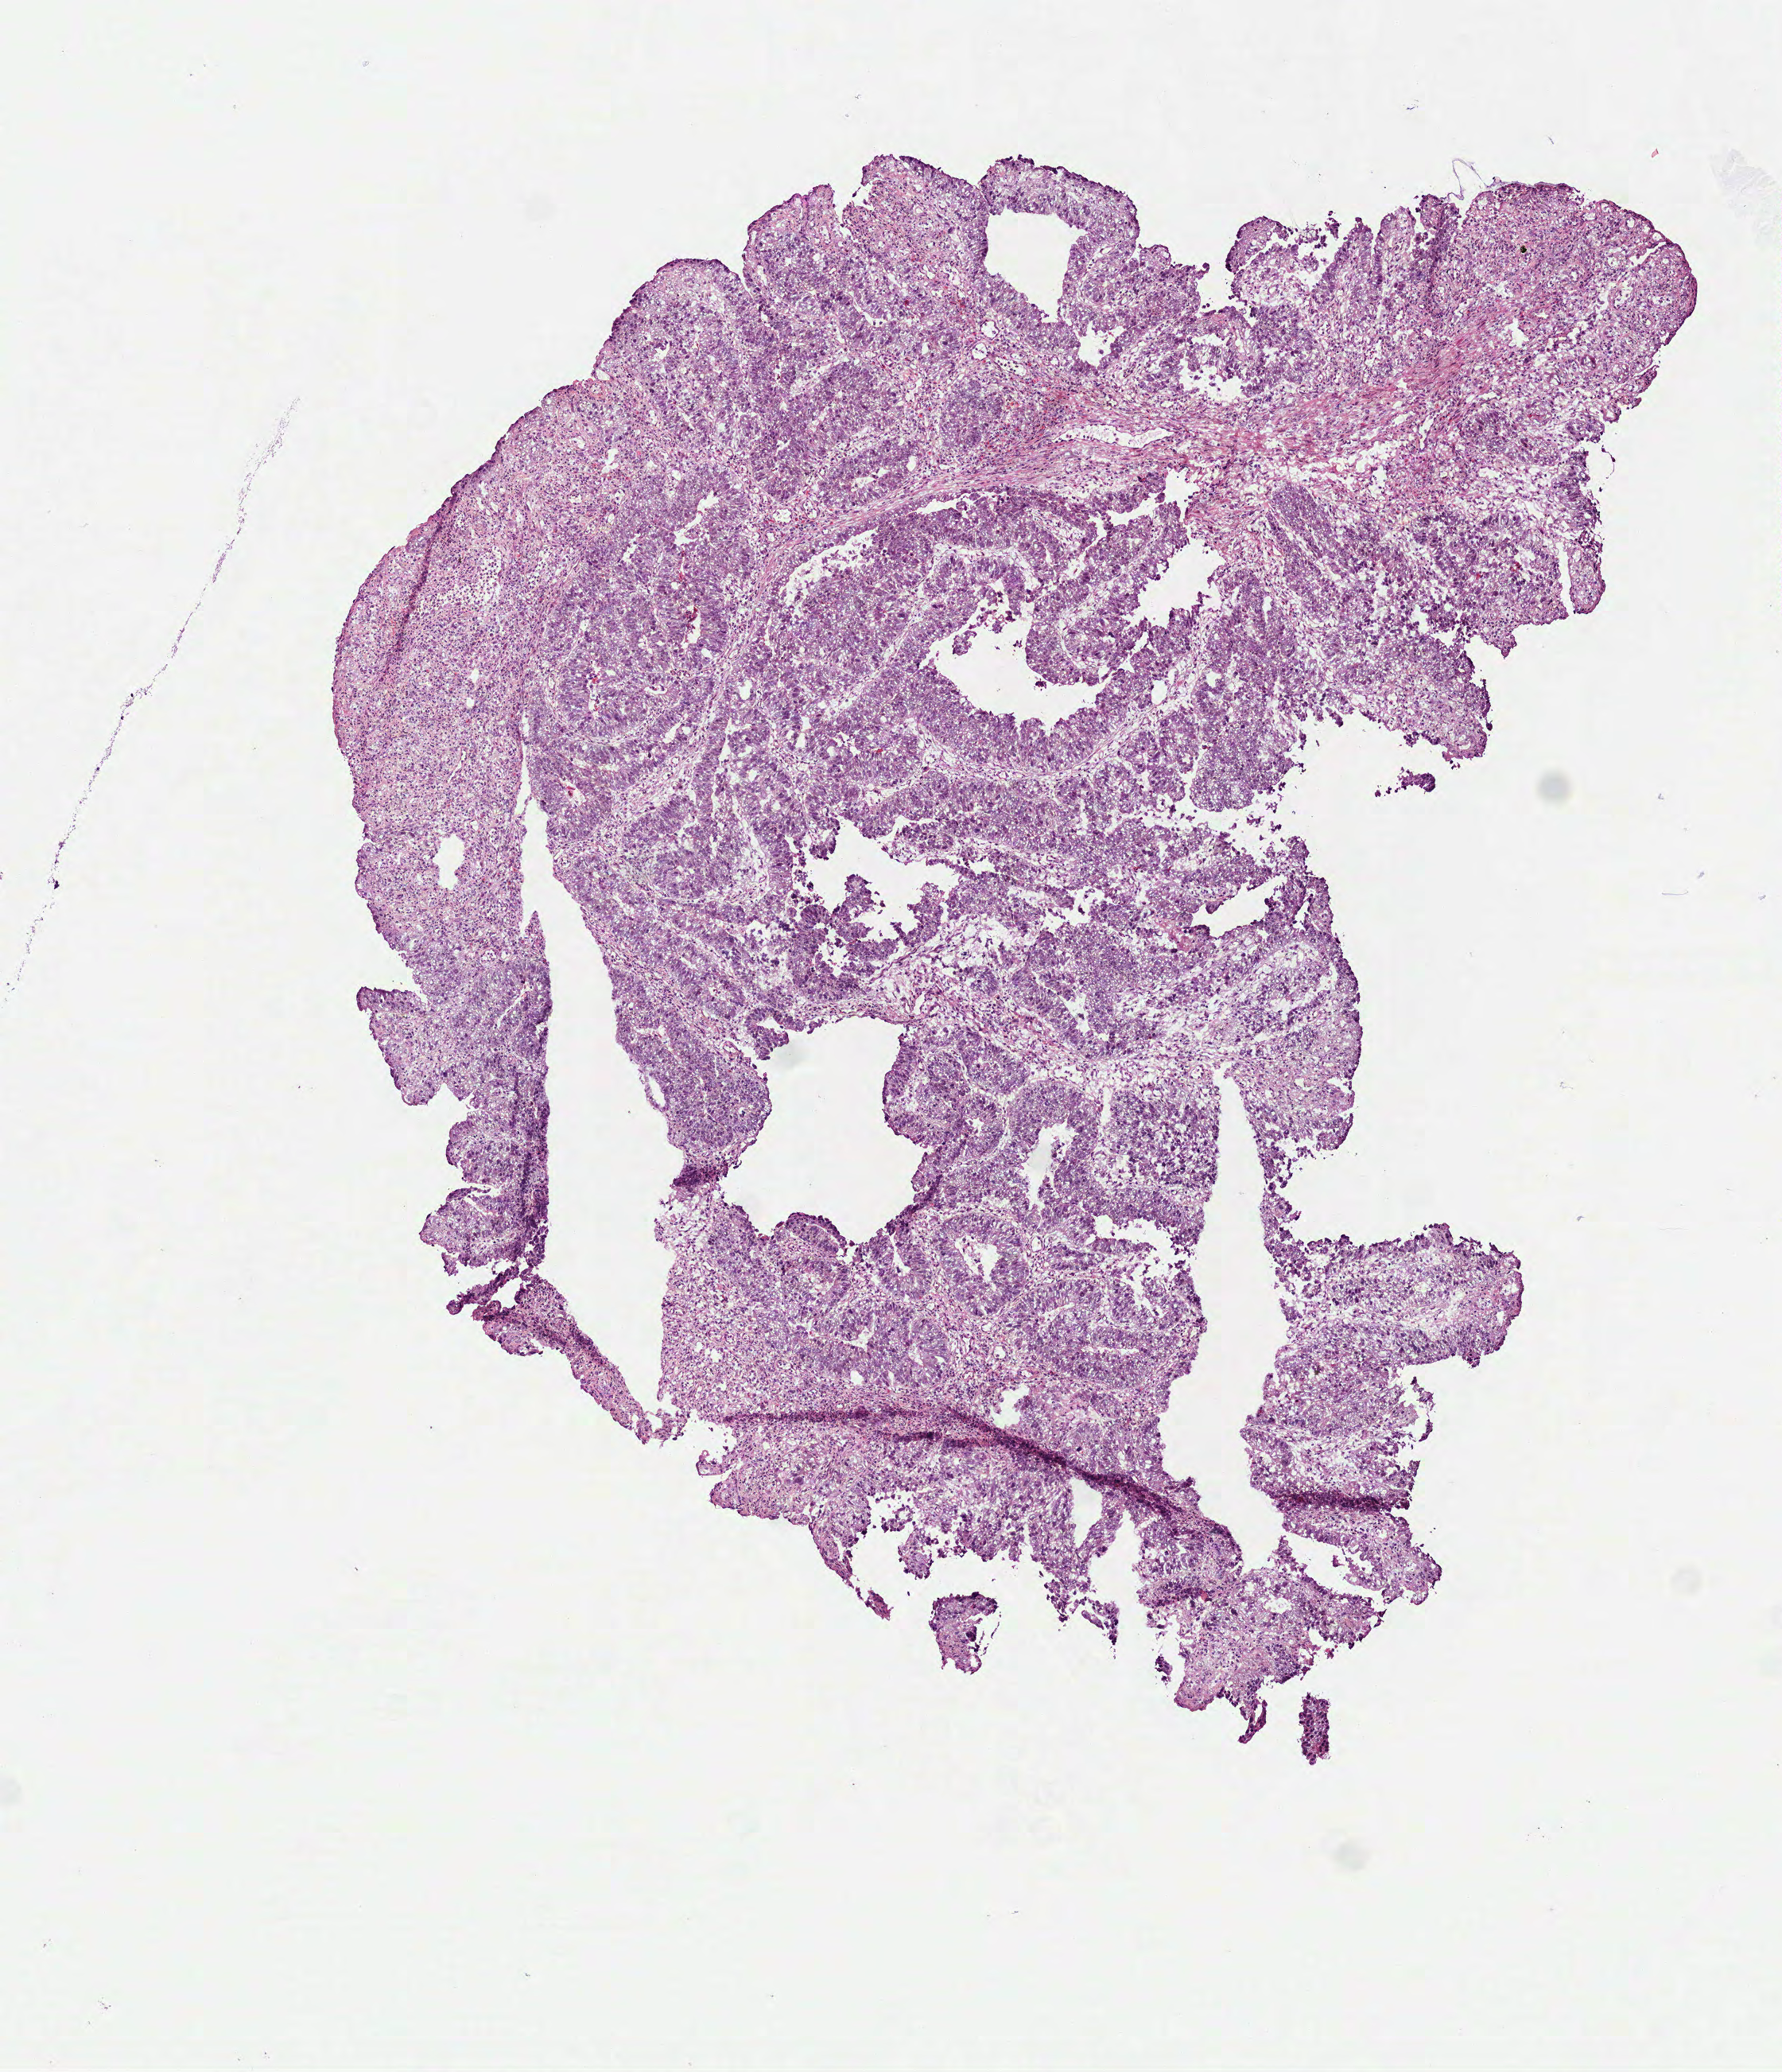
H&E whole-slide image — a low-resolution overview of the entire scanned area, about 4.5 x 5.3 mm (acquisition: 40x scan), frozen section from the top of the tissue portion, rectum, primary tumour sample. Patient: male, age at initial diagnosis 41 years. Composition of this section per pathologist review: tumour cells 95%, tumour nuclei 70%, normal cells 0%, stromal cells 5%, necrosis 0%.
Histologic diagnosis: Adenocarcinoma, NOS. AJCC pathologic stage: IV.